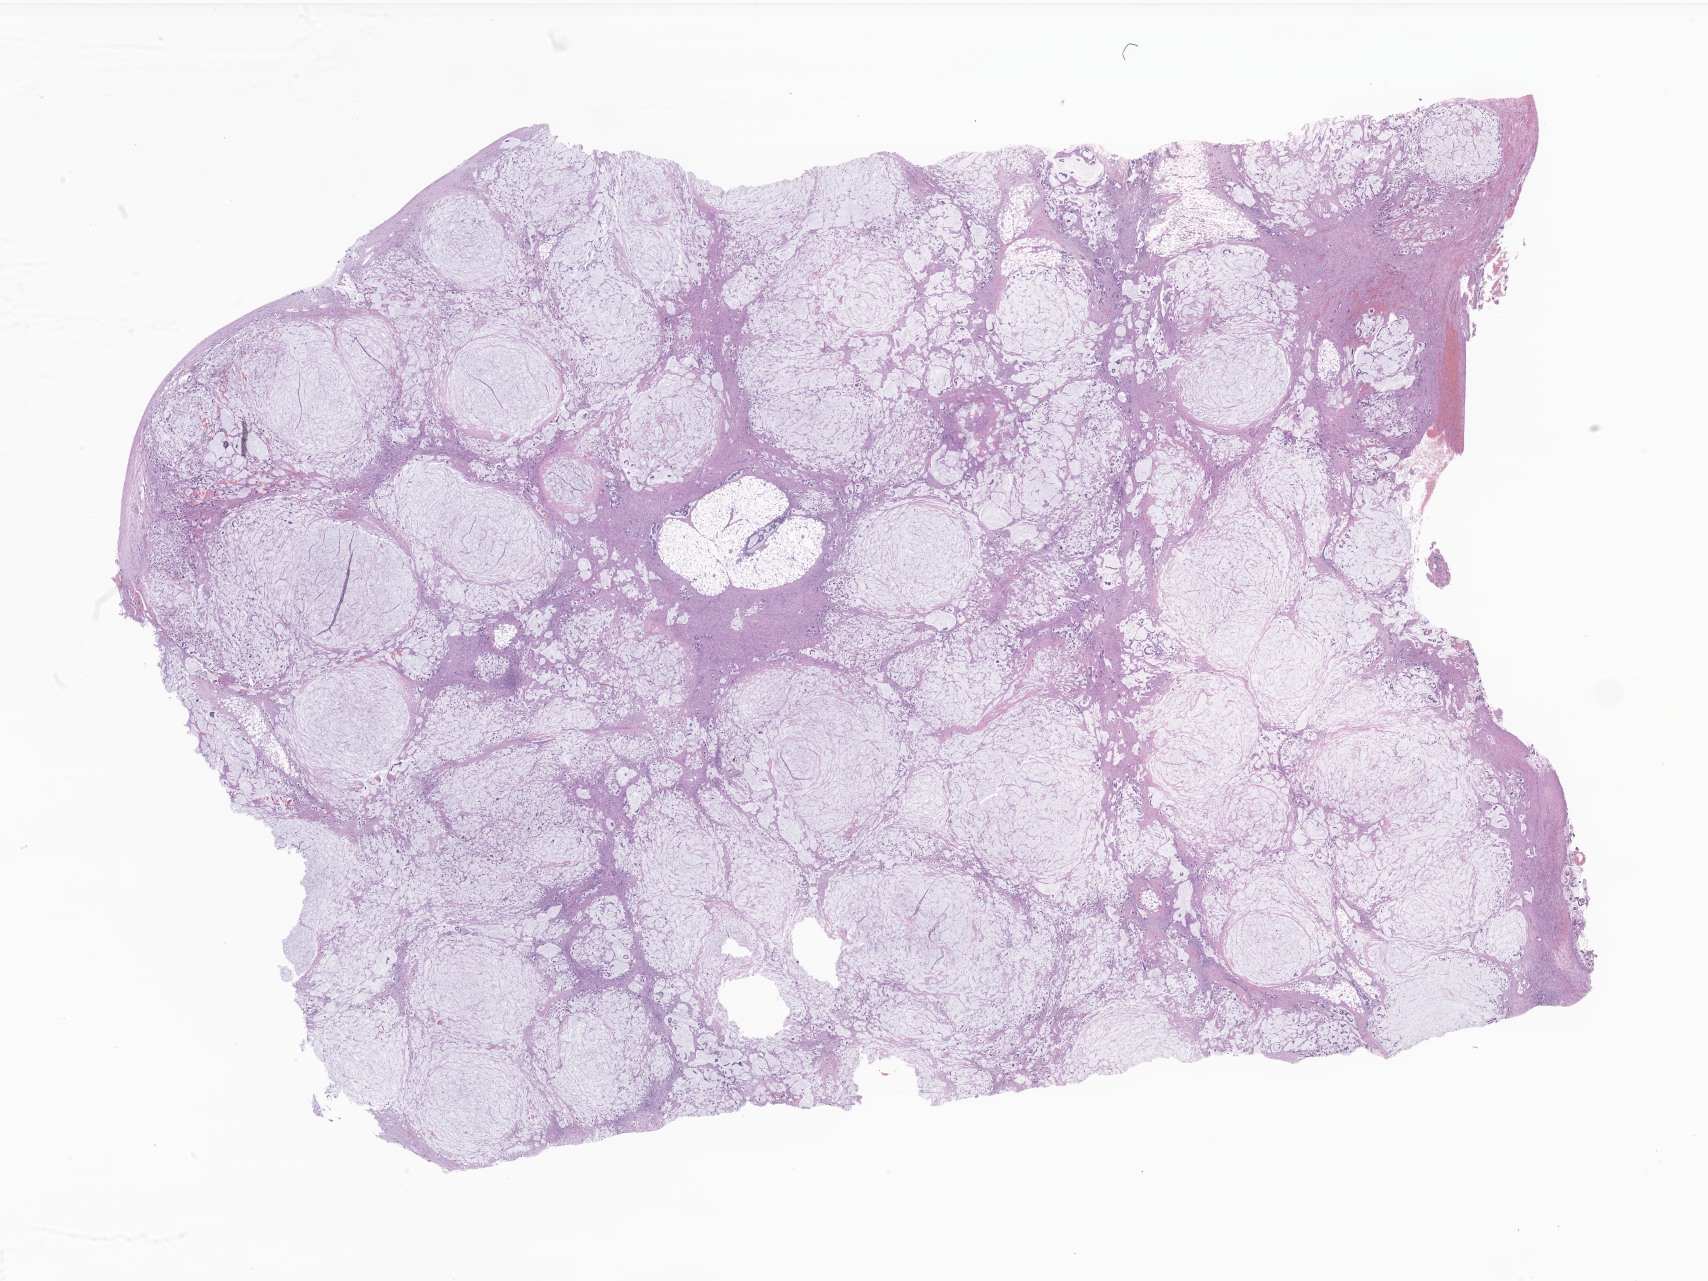
Whole-slide image, H&E stain of tumor tissue from the abdomen — low-resolution overview of the scanned area, about 28.8 x 21.6 mm, FFPE section. Patient: male, age 187 months.
Diagnosis (ICD-O-3 morphology term): Mucinous adenocarcinoma.